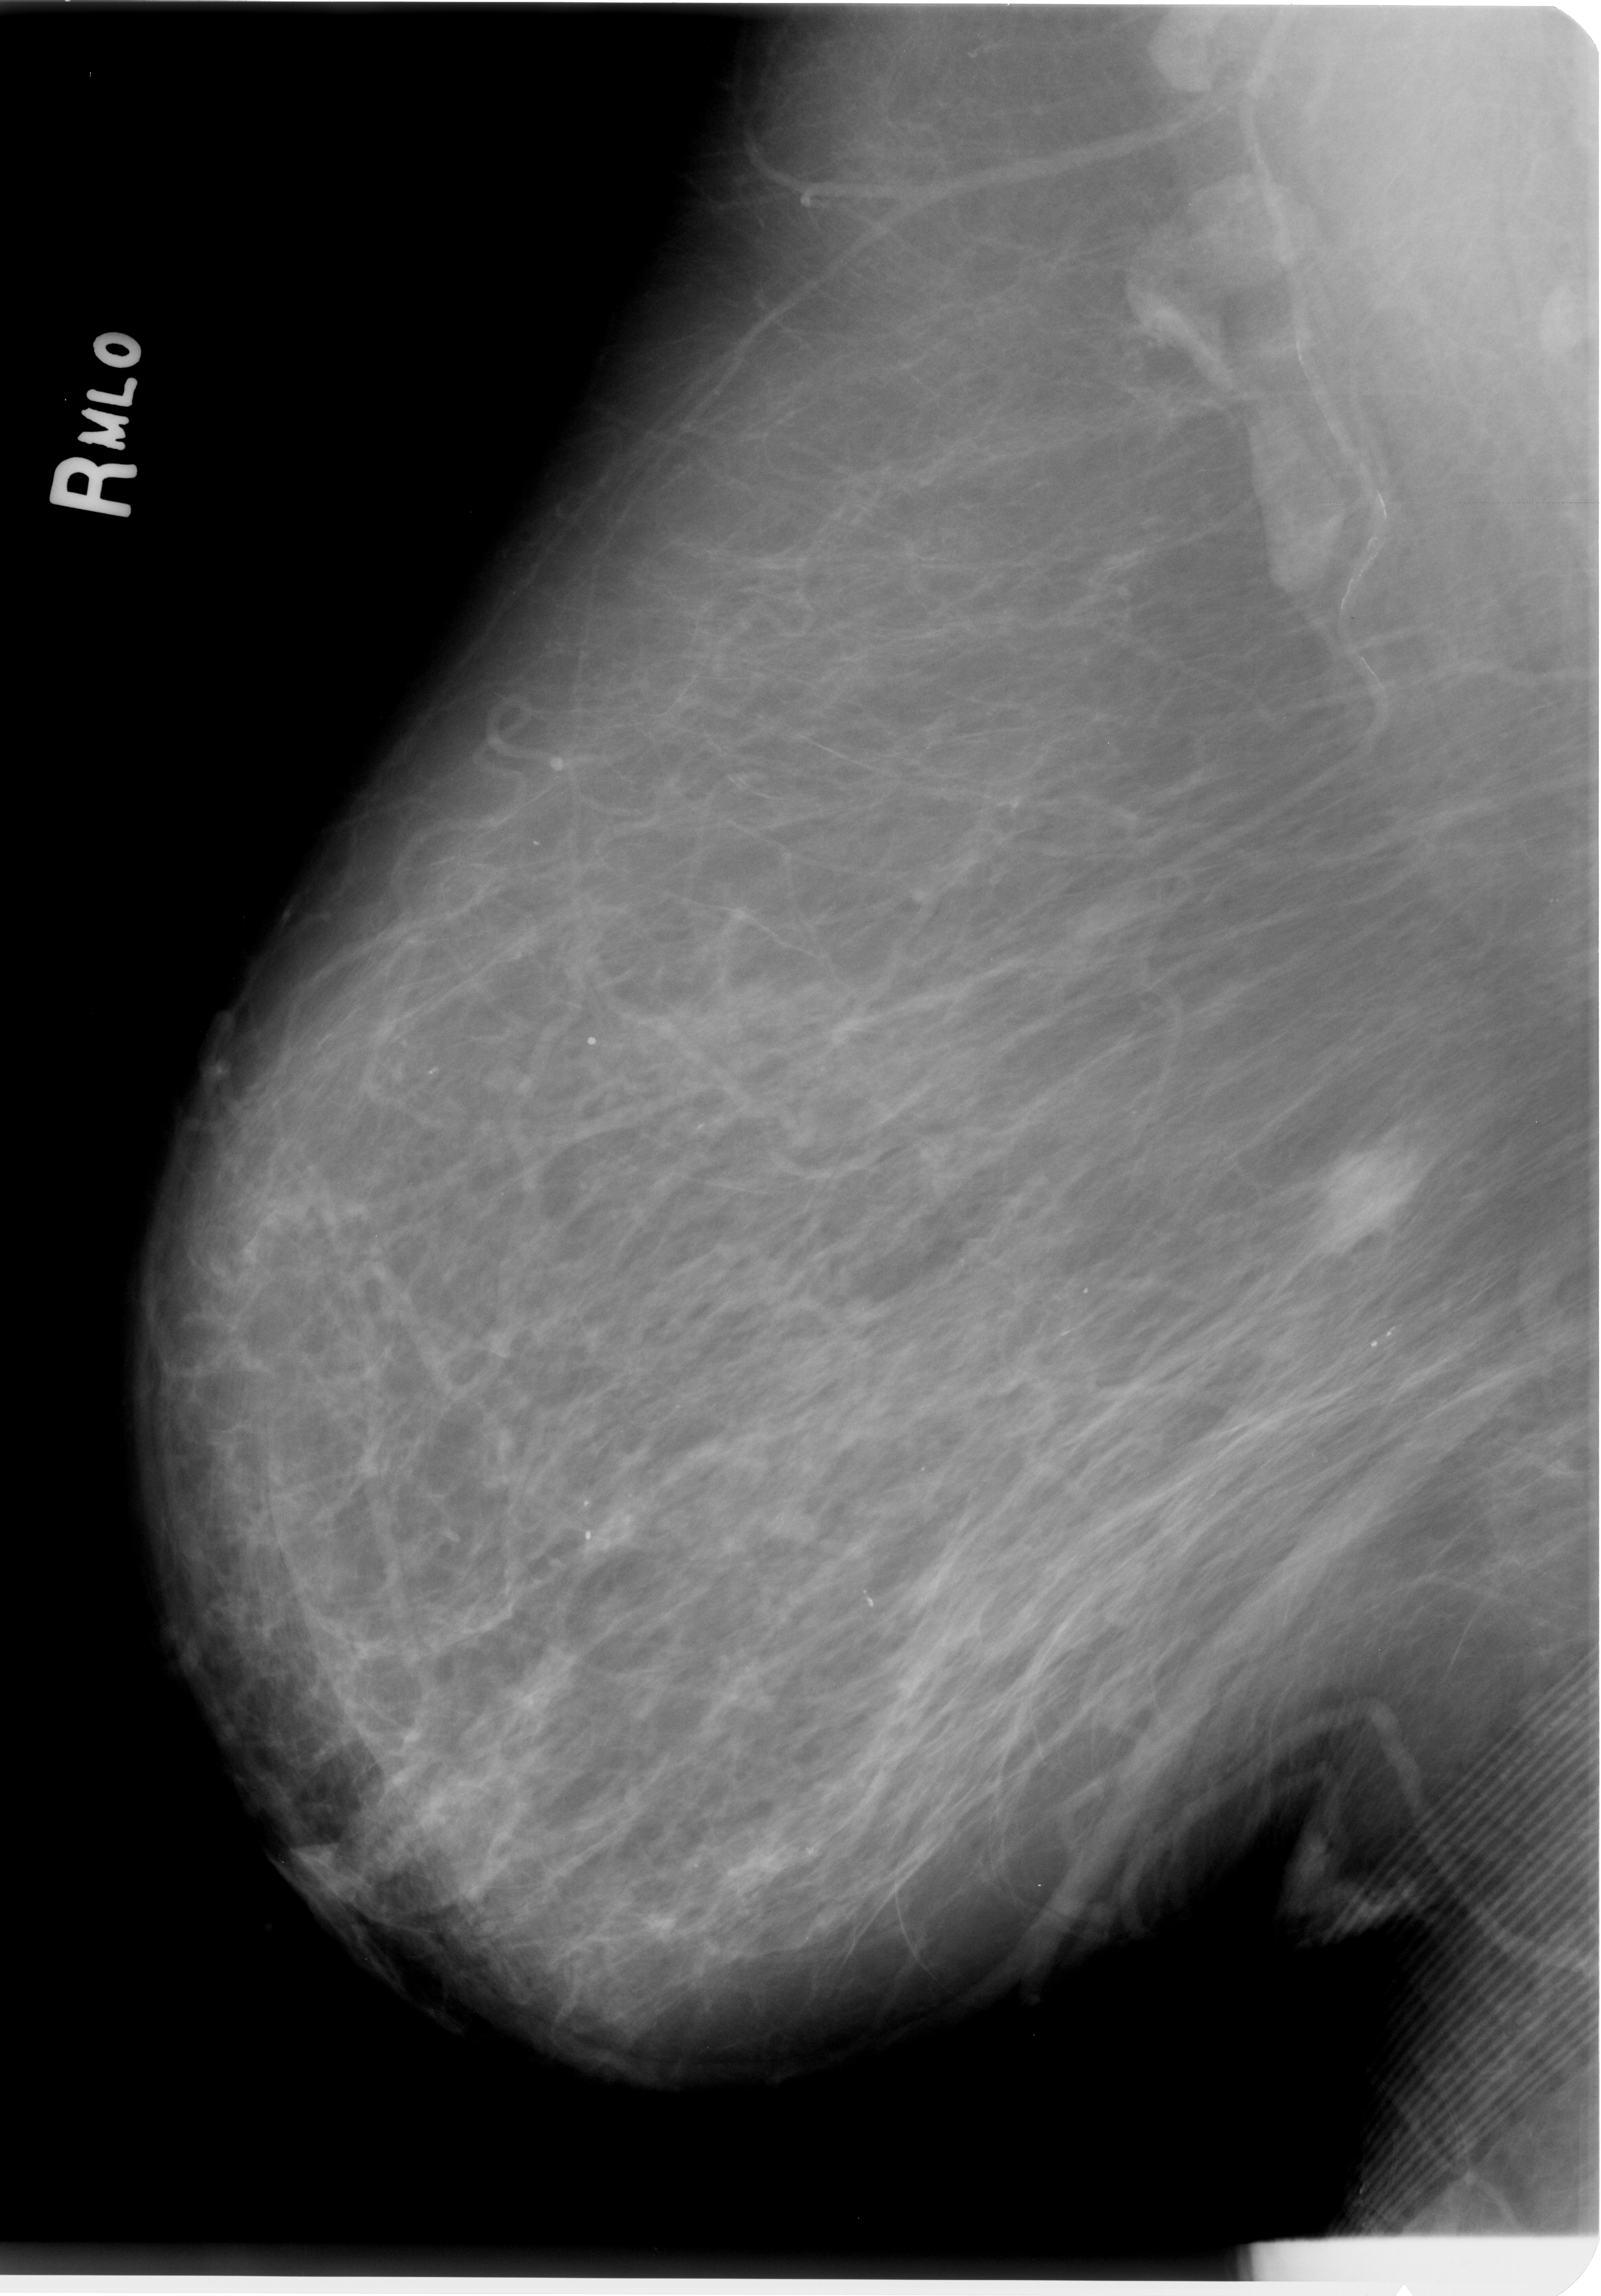
Digitized screen-film mammogram; right breast; mediolateral oblique (MLO) view; BI-RADS breast density category 2 (scale 1–4).
- Abnormality record for this image: mass, shape irregular, margins spiculated; BI-RADS assessment category 4; pathology (as recorded): malignant.